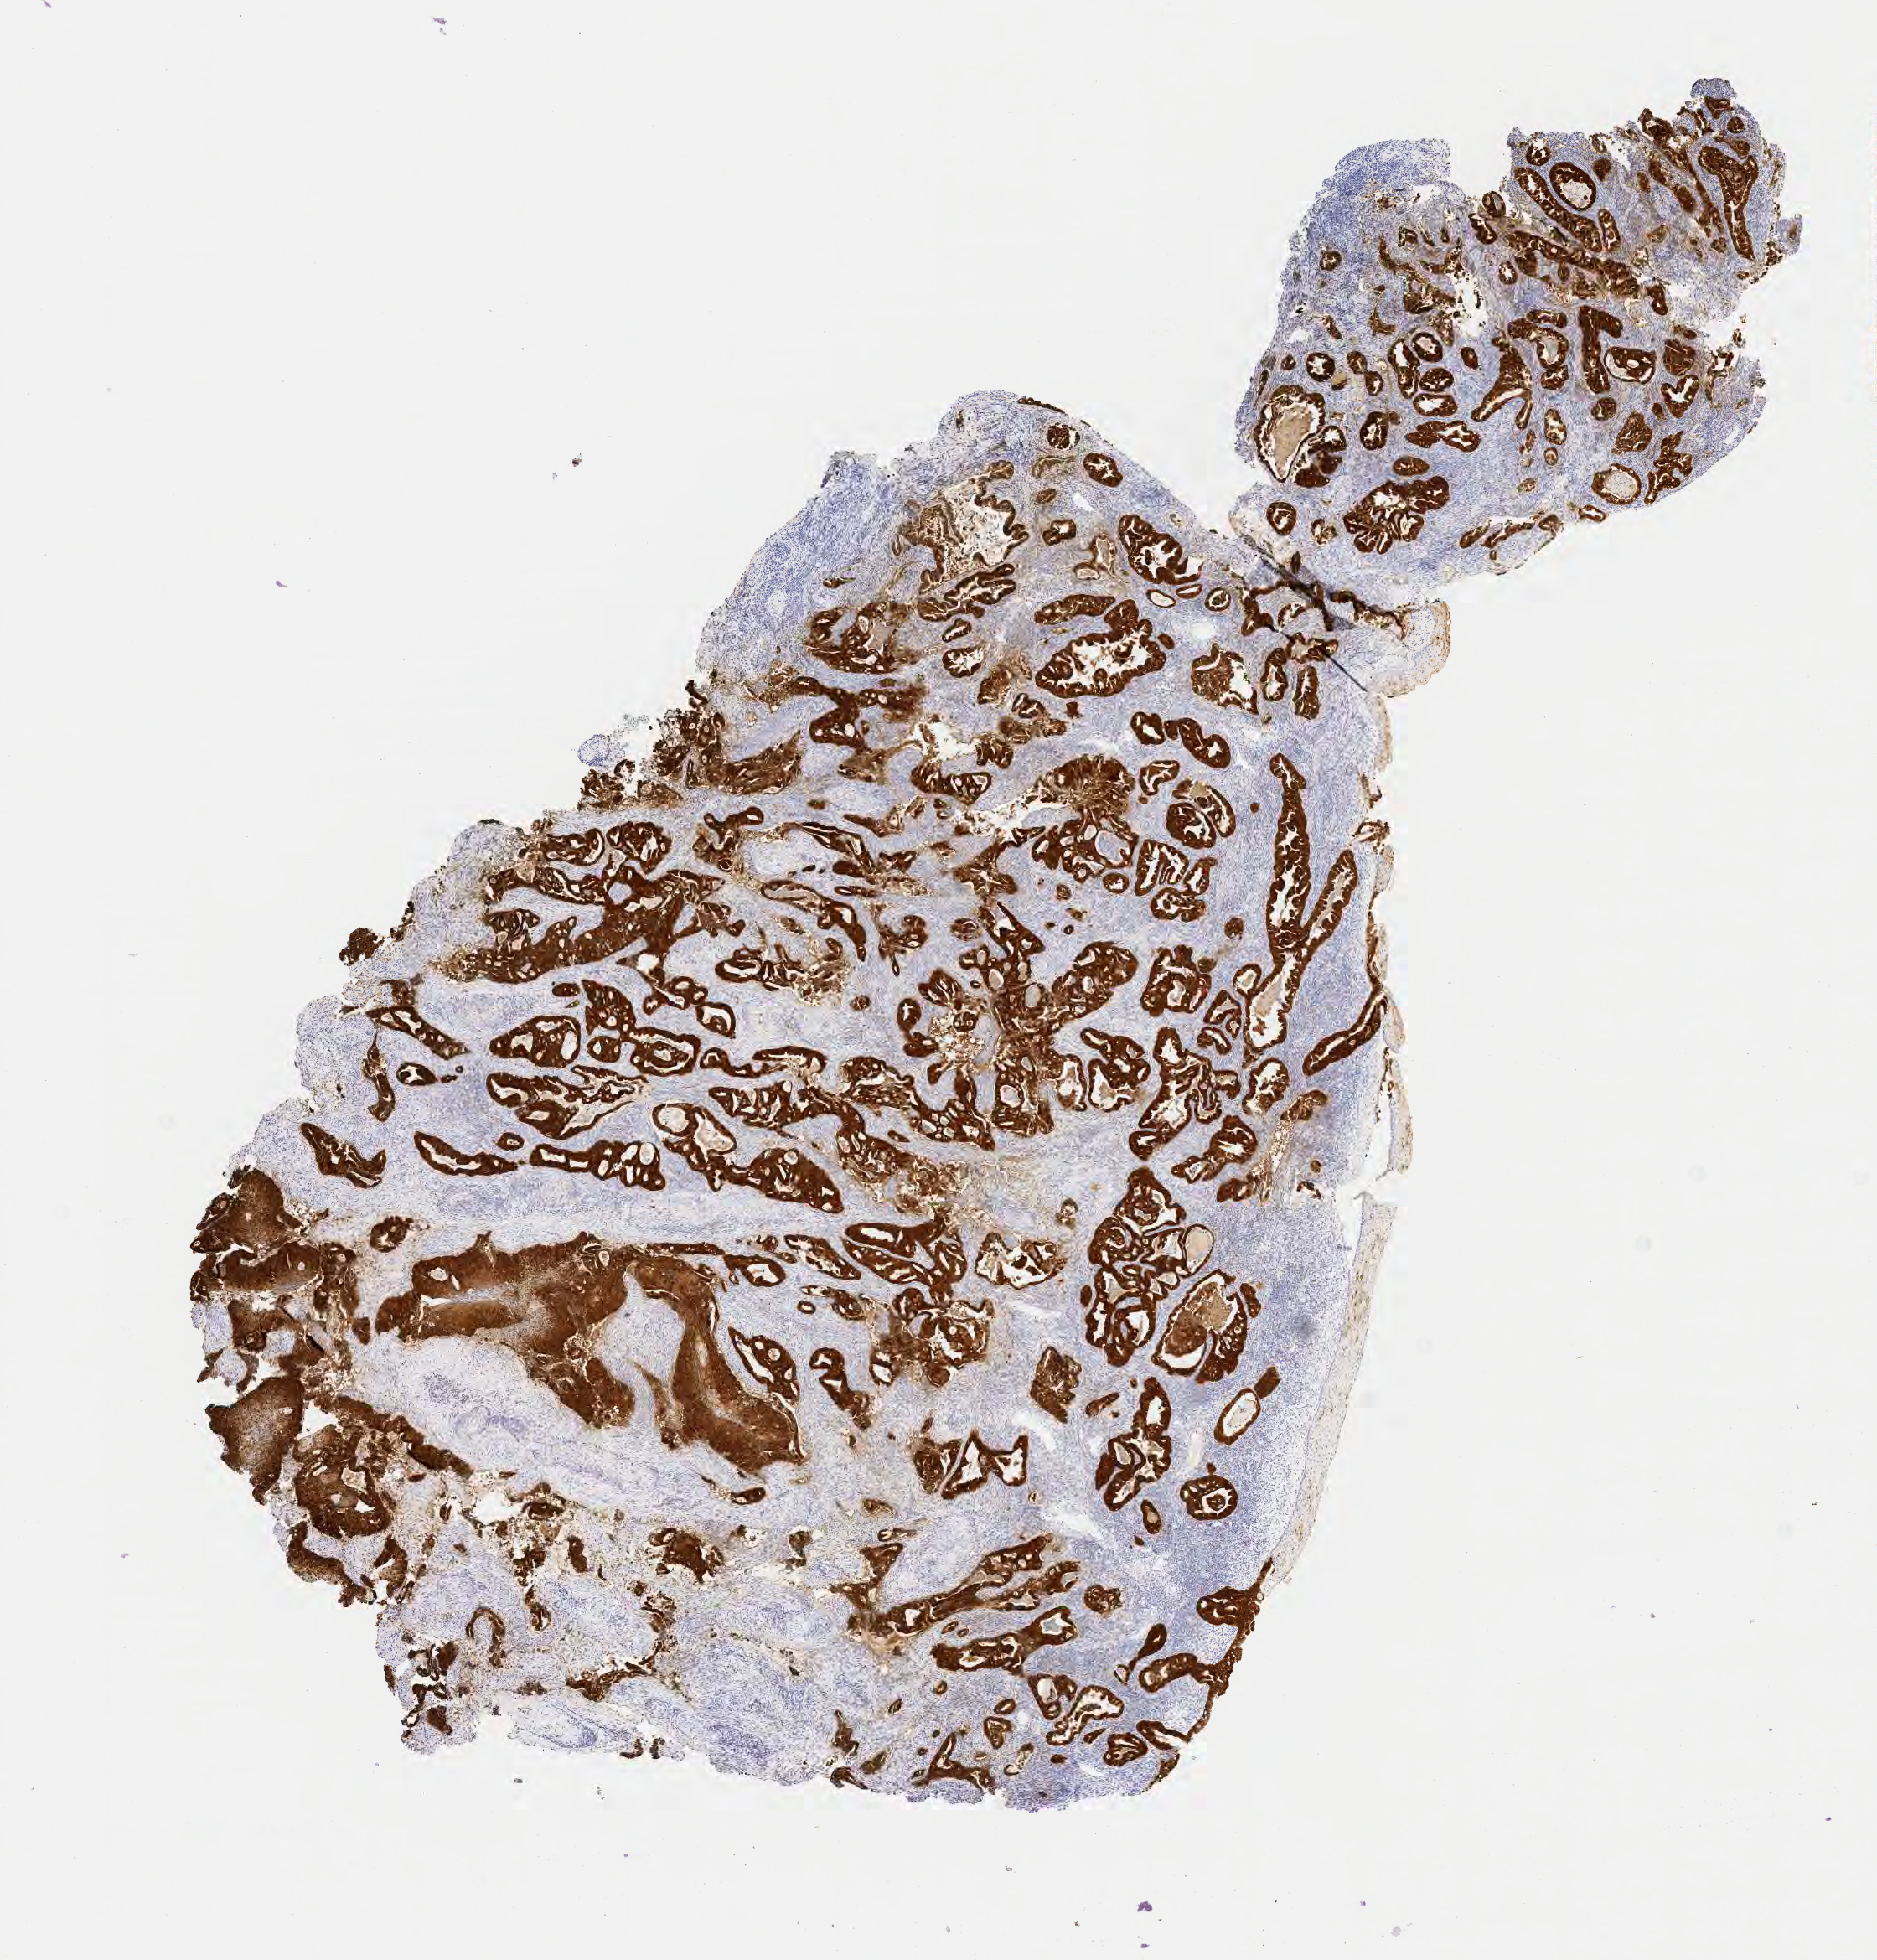
IHC for p16 (p16INK4a), whole-slide image — low-resolution overview of the scanned area, about 9.1 x 9.5 mm; tumor tissue; site: cervix. Patient: female, 56 years old.
Histologic diagnosis: Adenosquamous carcinoma.